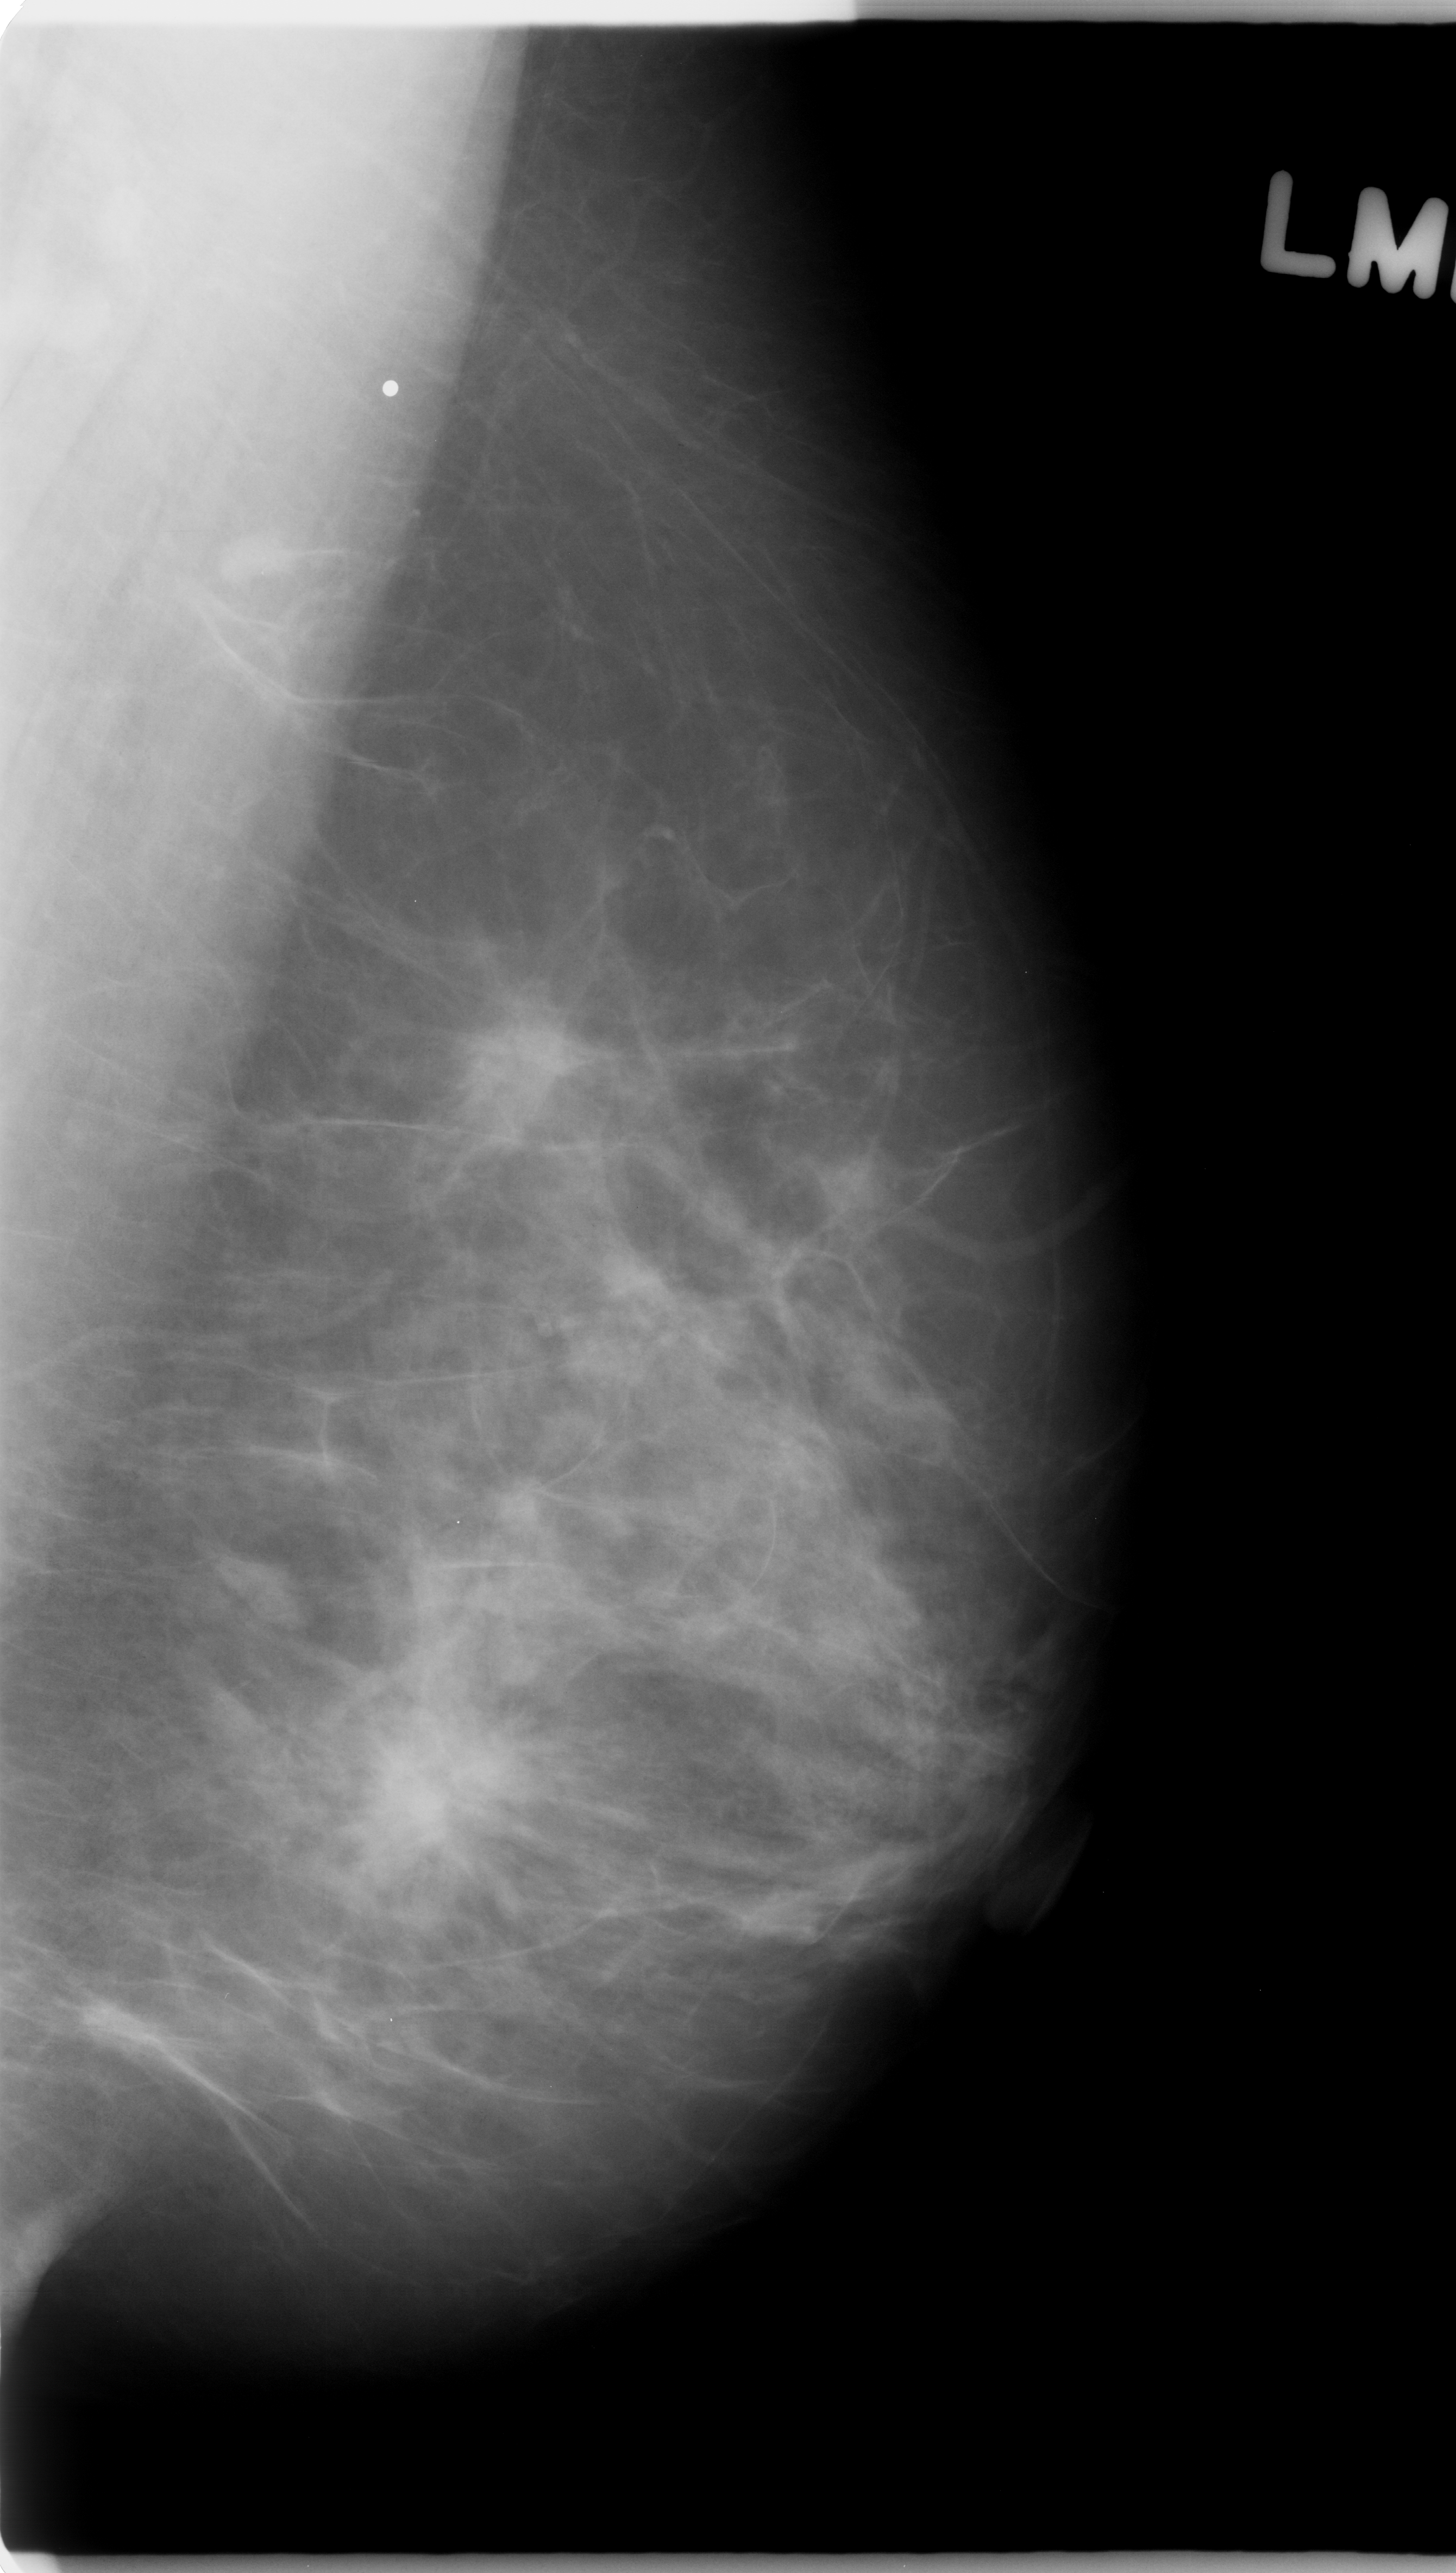
Scanned film-screen mammogram. Left breast. Mediolateral oblique (MLO) view. BI-RADS breast density category 2 (scale 1–4). 1456 × 2573 image matrix.
Expert-marked regions of interest on this image (one box per marked abnormality):
- Finding 1 of 2: mass, shape architectural distortion, margins spiculated; BI-RADS assessment category 5; pathology result (as recorded, not read from the image): malignant: bounding box [x1, y1, x2, y2] px = [305, 1622, 535, 1874]
- Finding 2 of 2: mass, shape architectural distortion, margins spiculated; BI-RADS assessment category 5; pathology (as recorded): malignant: [429, 924, 624, 1144]